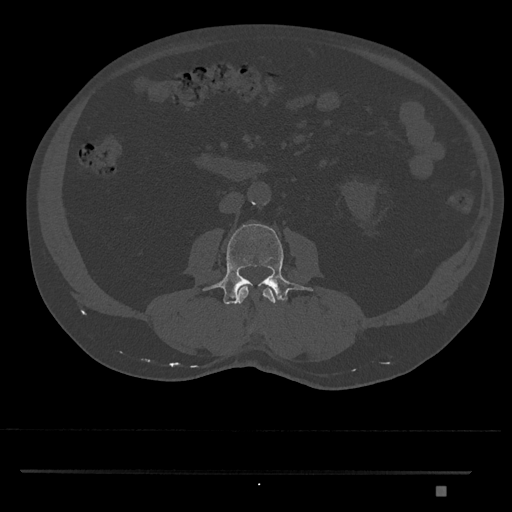
CT including the spine, one axial slice; slice 698 of 1134 in the series (ordered by position); reconstruction kernel Br40s/3; 120 kVp; bone window (W 1800 / L 400 HU); 0.5 mm slice thickness; 512 × 512 image matrix, field of view 429 × 429 mm. Male patient, age 65 years. From the clinical record (not read from this slice): primary cancer: prostate.
Outlined on this slice (semi-automatic segmentation, software-assisted and operator-edited):
- L2 vertebra: bounding box <237,285,276,325> (left, top, right, bottom; pixels)
- L3 vertebra: <203,223,313,305>